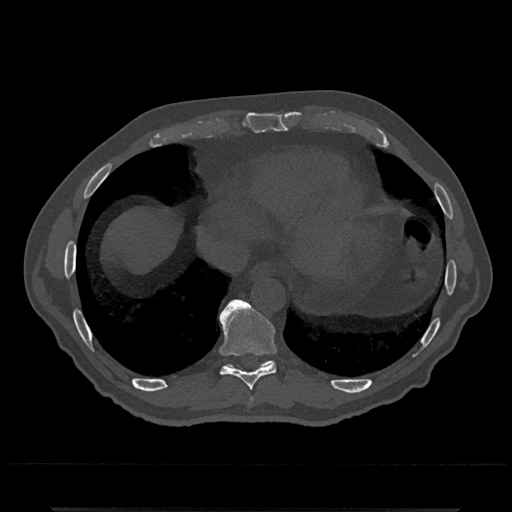
CT including the spine, one axial slice; slice 601 of 797 in the series (ordered by position); 120 kVp; bone window (W 1800 / L 400 HU); 0.5 mm slice thickness; 512 × 512 image matrix, field of view 393 × 393 mm. Patient: male, 67 years. Case-level facts recorded for this patient, not image findings: primary cancer: prostate.
Annotated regions visible in this slice (semi-automatic segmentation, software-assisted and operator-edited):
- T10 vertebra: box from (x=227, y=299) to (x=275, y=366) px
- T9 vertebra: (x=219, y=299)–(x=276, y=391)